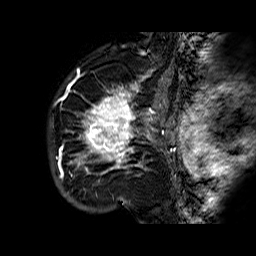
Breast MRI (dynamic contrast-enhanced), one sagittal slice. Position 49 of 60 along the scan axis. Dynamic contrast-enhanced series, time point 2 of 6 at this slice position (early post-contrast). 1.5 T. TE 6.3 ms, TR 32.4 ms. 4 mm slice thickness. 256 × 256 image matrix, field of view 200 × 200 mm. Female patient. Case-level facts recorded for this patient, not image findings: setting: breast cancer imaged before/during neoadjuvant chemotherapy; receptor status: HR-positive, HER2-negative.
Annotated regions visible in this slice (semi-automatically segmented with operator editing):
- analysis volume of interest (the breast-tissue region the enhancement analysis was run in; not a lesion): bounding box [x1, y1, x2, y2] px = [68, 72, 177, 183]
- tumour enhancement mask (voxels above the 100 % enhancement threshold inside the analysis volume of interest): [70, 73, 175, 175]